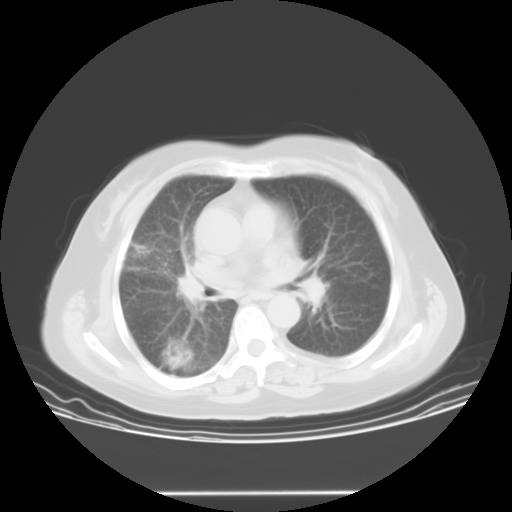
Chest CT, one axial slice; position 13 of 23 along the scan axis; 120 kVp; lung window (W 1500 / L -600 HU); 10 mm slice thickness; 512 × 512 image matrix, field of view 408 × 408 mm. Female patient, age 55 years. From the clinical record (not read from this slice): clinical TNM (as recorded): T2 N0 M1b.
Annotated regions visible in this slice (bounding box drawn by a radiologist):
- lung tumour (recorded histology: squamous cell carcinoma): box from (x=164, y=348) to (x=178, y=361) px